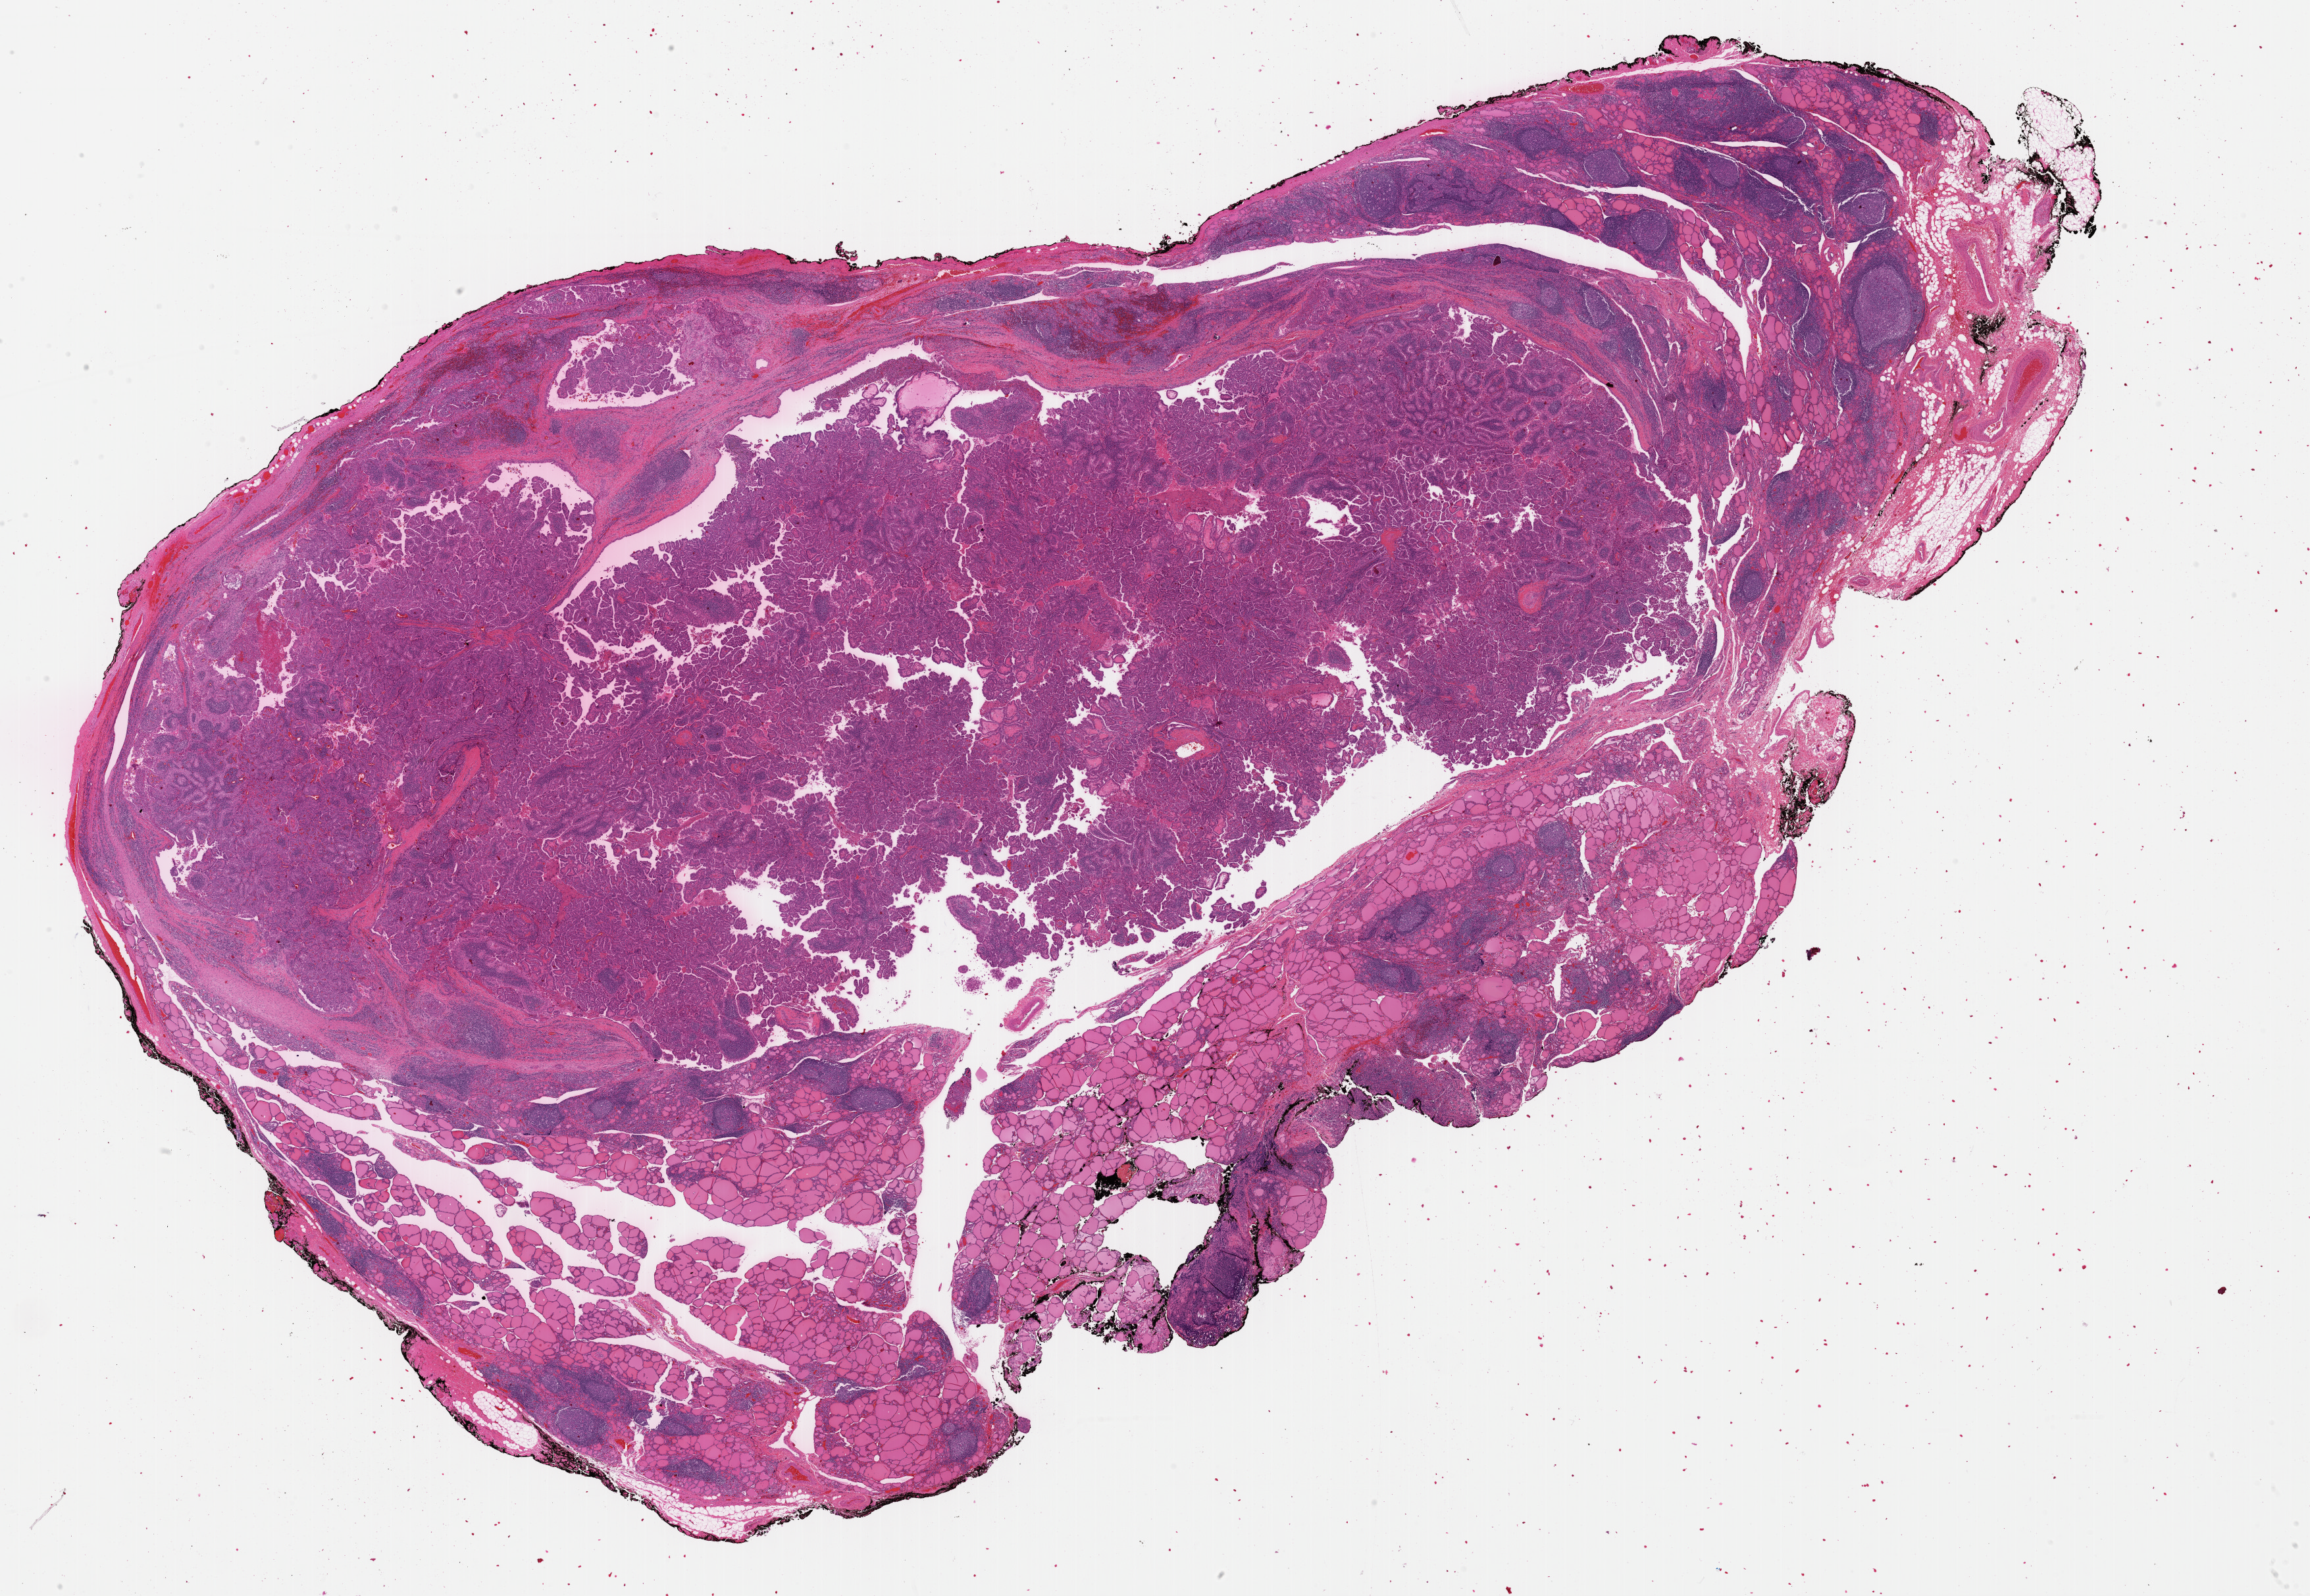
Digitized Hematoxylin and eosin (H&E) stained tissue section (whole slide), shown as a low-resolution overview of the whole scanned area (about 27.7 x 19.2 mm, from a 40x scan), formalin-fixed paraffin-embedded (FFPE) diagnostic section, thyroid, primary tumour sample. Patient: female, age at initial diagnosis 33 years.
TNM: T2 NX MX. Diagnosis: Papillary adenocarcinoma, NOS (thyroid gland). Laterality: right. AJCC pathologic stage: I.